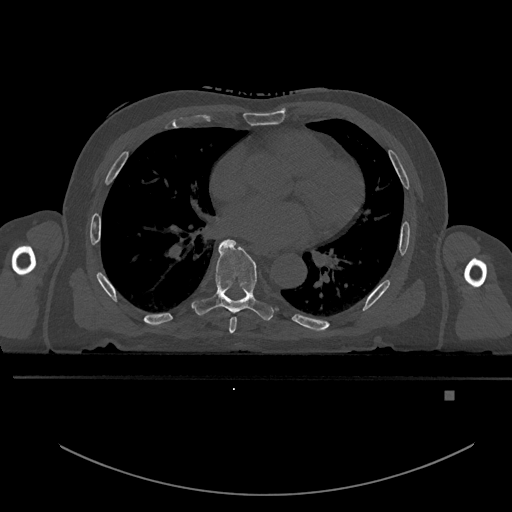
CT including the spine, one axial slice; position 260 of 969 along the scan axis; bone window (W 1800 / L 400 HU); 0.5 mm slice thickness; 512 × 512 image matrix, field of view 456 × 456 mm. Male patient, age 82 years. Case-level facts recorded for this patient, not image findings: primary cancer: prostate; vertebrae with lytic lesions (as recorded): T11, T9, T8, T2.
Outlined on this slice (semi-automatically segmented with operator editing):
- T6 vertebra: bounding box [x1, y1, x2, y2] px = [229, 317, 237, 334]
- T7 vertebra: [192, 239, 273, 321]